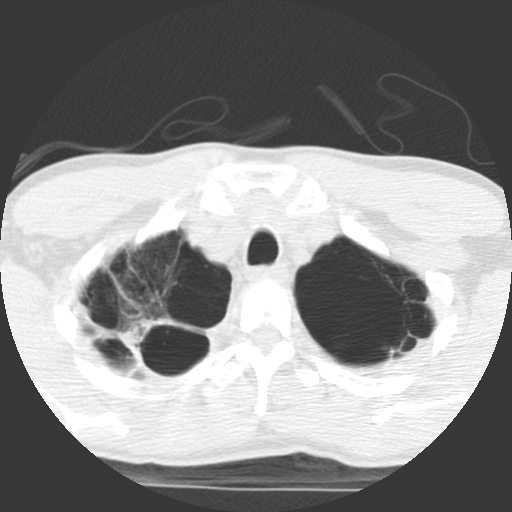
Chest CT (low-dose screening protocol), one axial image. Baseline screening round. Lung window (W 1500 / L -600 HU). Standard (soft-tissue) reconstruction kernel (STANDARD). Slice 97 of 117 in the series. 512 × 512 image matrix. Male, age 62 years at enrolment.
Expert-annotated lung lesion, bounding box [x1, y1, x2, y2] px = [108, 299, 215, 387]. Screening reader's record for this exam: no non-calcified nodule ≥4 mm recorded. Official screen result: negative screen, minor abnormalities not suspicious for lung cancer. Participant outcome: lung cancer diagnosed 357 days after this screen — non-small cell carcinoma, right upper lobe, poorly differentiated (G3), stage IA (AJCC 6th edition), 70 mm at pathology.